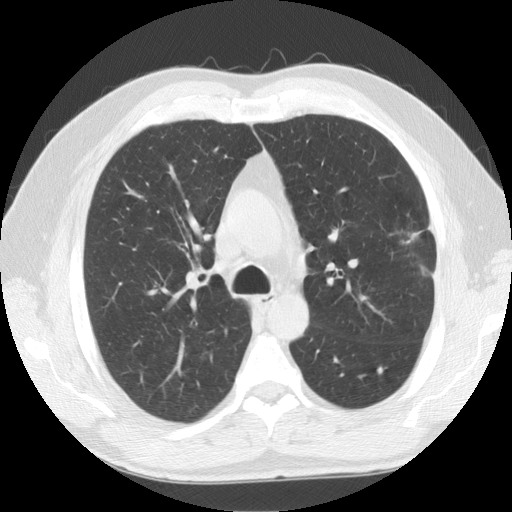
Low-dose screening chest CT, axial slice; baseline screening round; lung window (W 1500 / L -600 HU); 2.5 mm slice thickness; 512 × 512 image matrix. Male participant, aged 59 years at enrolment. Former smoker at enrolment.
Expert-annotated lung lesion, bounding box (x1, y1, x2, y2) in pixels: (369, 204, 452, 282). Screening reader's record for this exam (one nodule recorded; not confirmed to be the boxed lesion): non-calcified nodule or mass ≥4 mm, left upper lobe, 23 × 23 mm, spiculated (stellate) margins, soft tissue attenuation. Later outcome: lung cancer diagnosed 28 days after this screen — squamous cell carcinoma, NOS, left upper lobe, moderately differentiated (G2), stage IA (AJCC 6th edition), 27 mm at pathology.